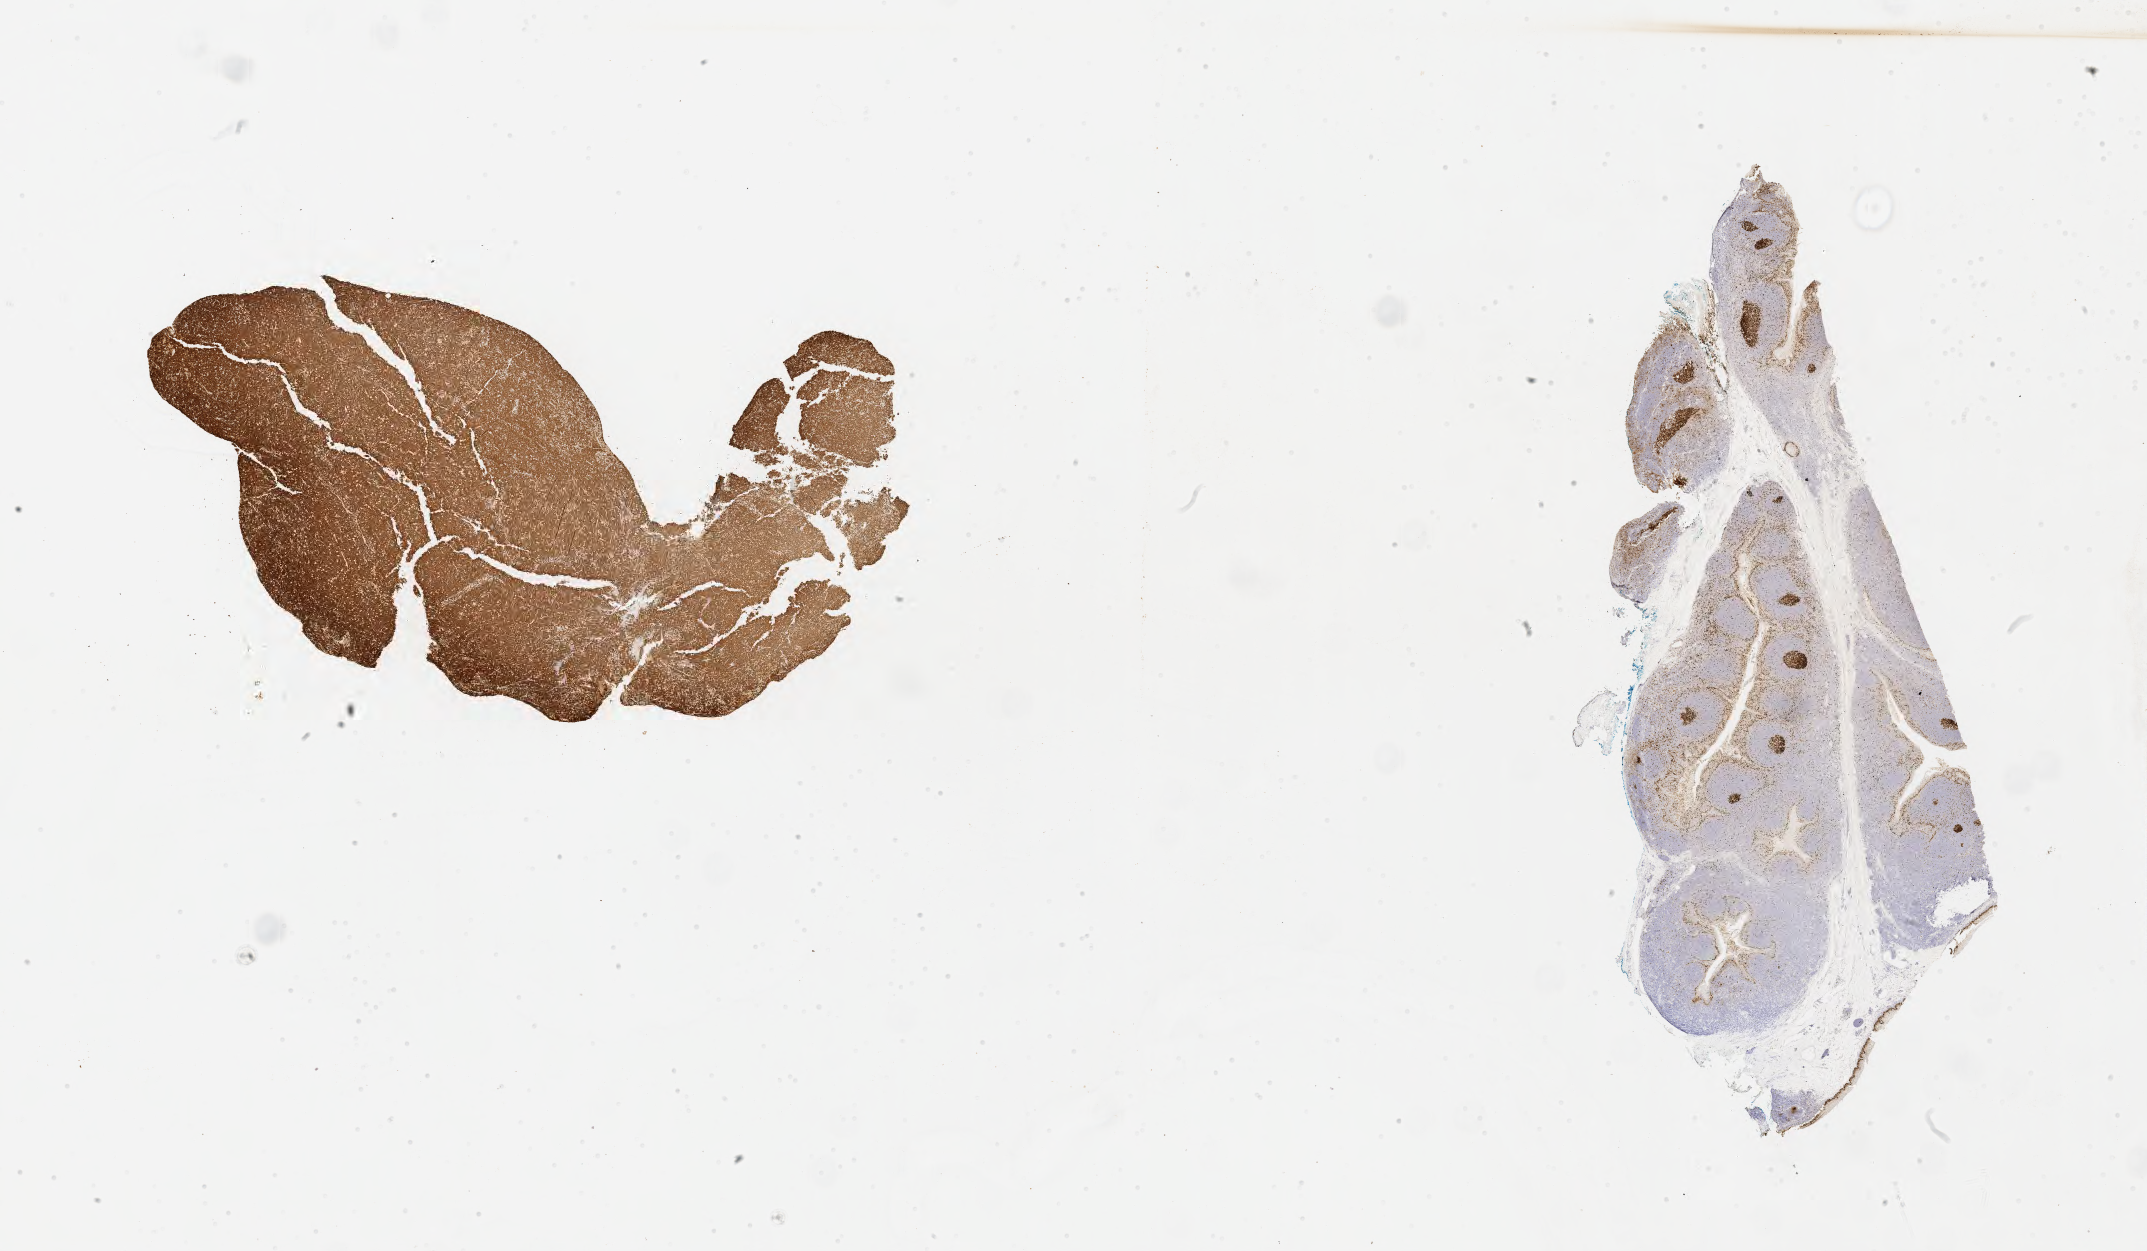
Whole-slide image, immunohistochemical stain for Ki-67 — low-resolution overview of the scanned area, about 34.7 x 20.2 mm. Specimen: tumor tissue. Site: lymph node of head and neck. Male patient; age at initial diagnosis 5 years.
Diagnosis: Burkitt lymphoma, NOS.